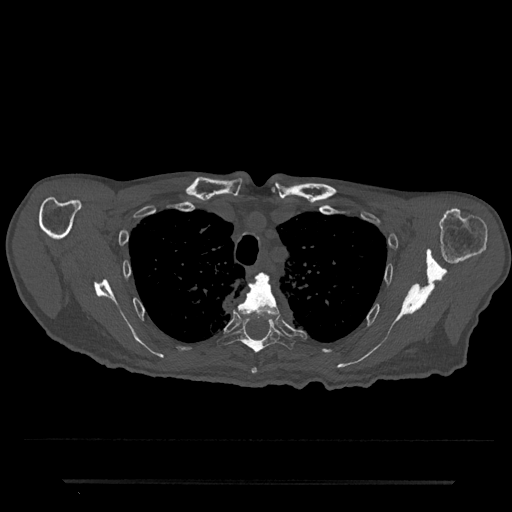
CT including the spine, one axial slice; position 596 of 797 along the scan axis; bone window (W 1800 / L 400 HU); 0.5 mm slice thickness; 512 × 512 image matrix, field of view 427 × 427 mm. Patient: male, 74 years. Case-level facts recorded for this patient, not image findings: primary cancer: prostate.
Outlined on this slice (semi-automatically segmented with operator editing):
- T4 vertebra: bounding box (x1, y1, x2, y2) in pixels: (237, 274, 280, 374)
- T5 vertebra: (217, 316, 295, 353)